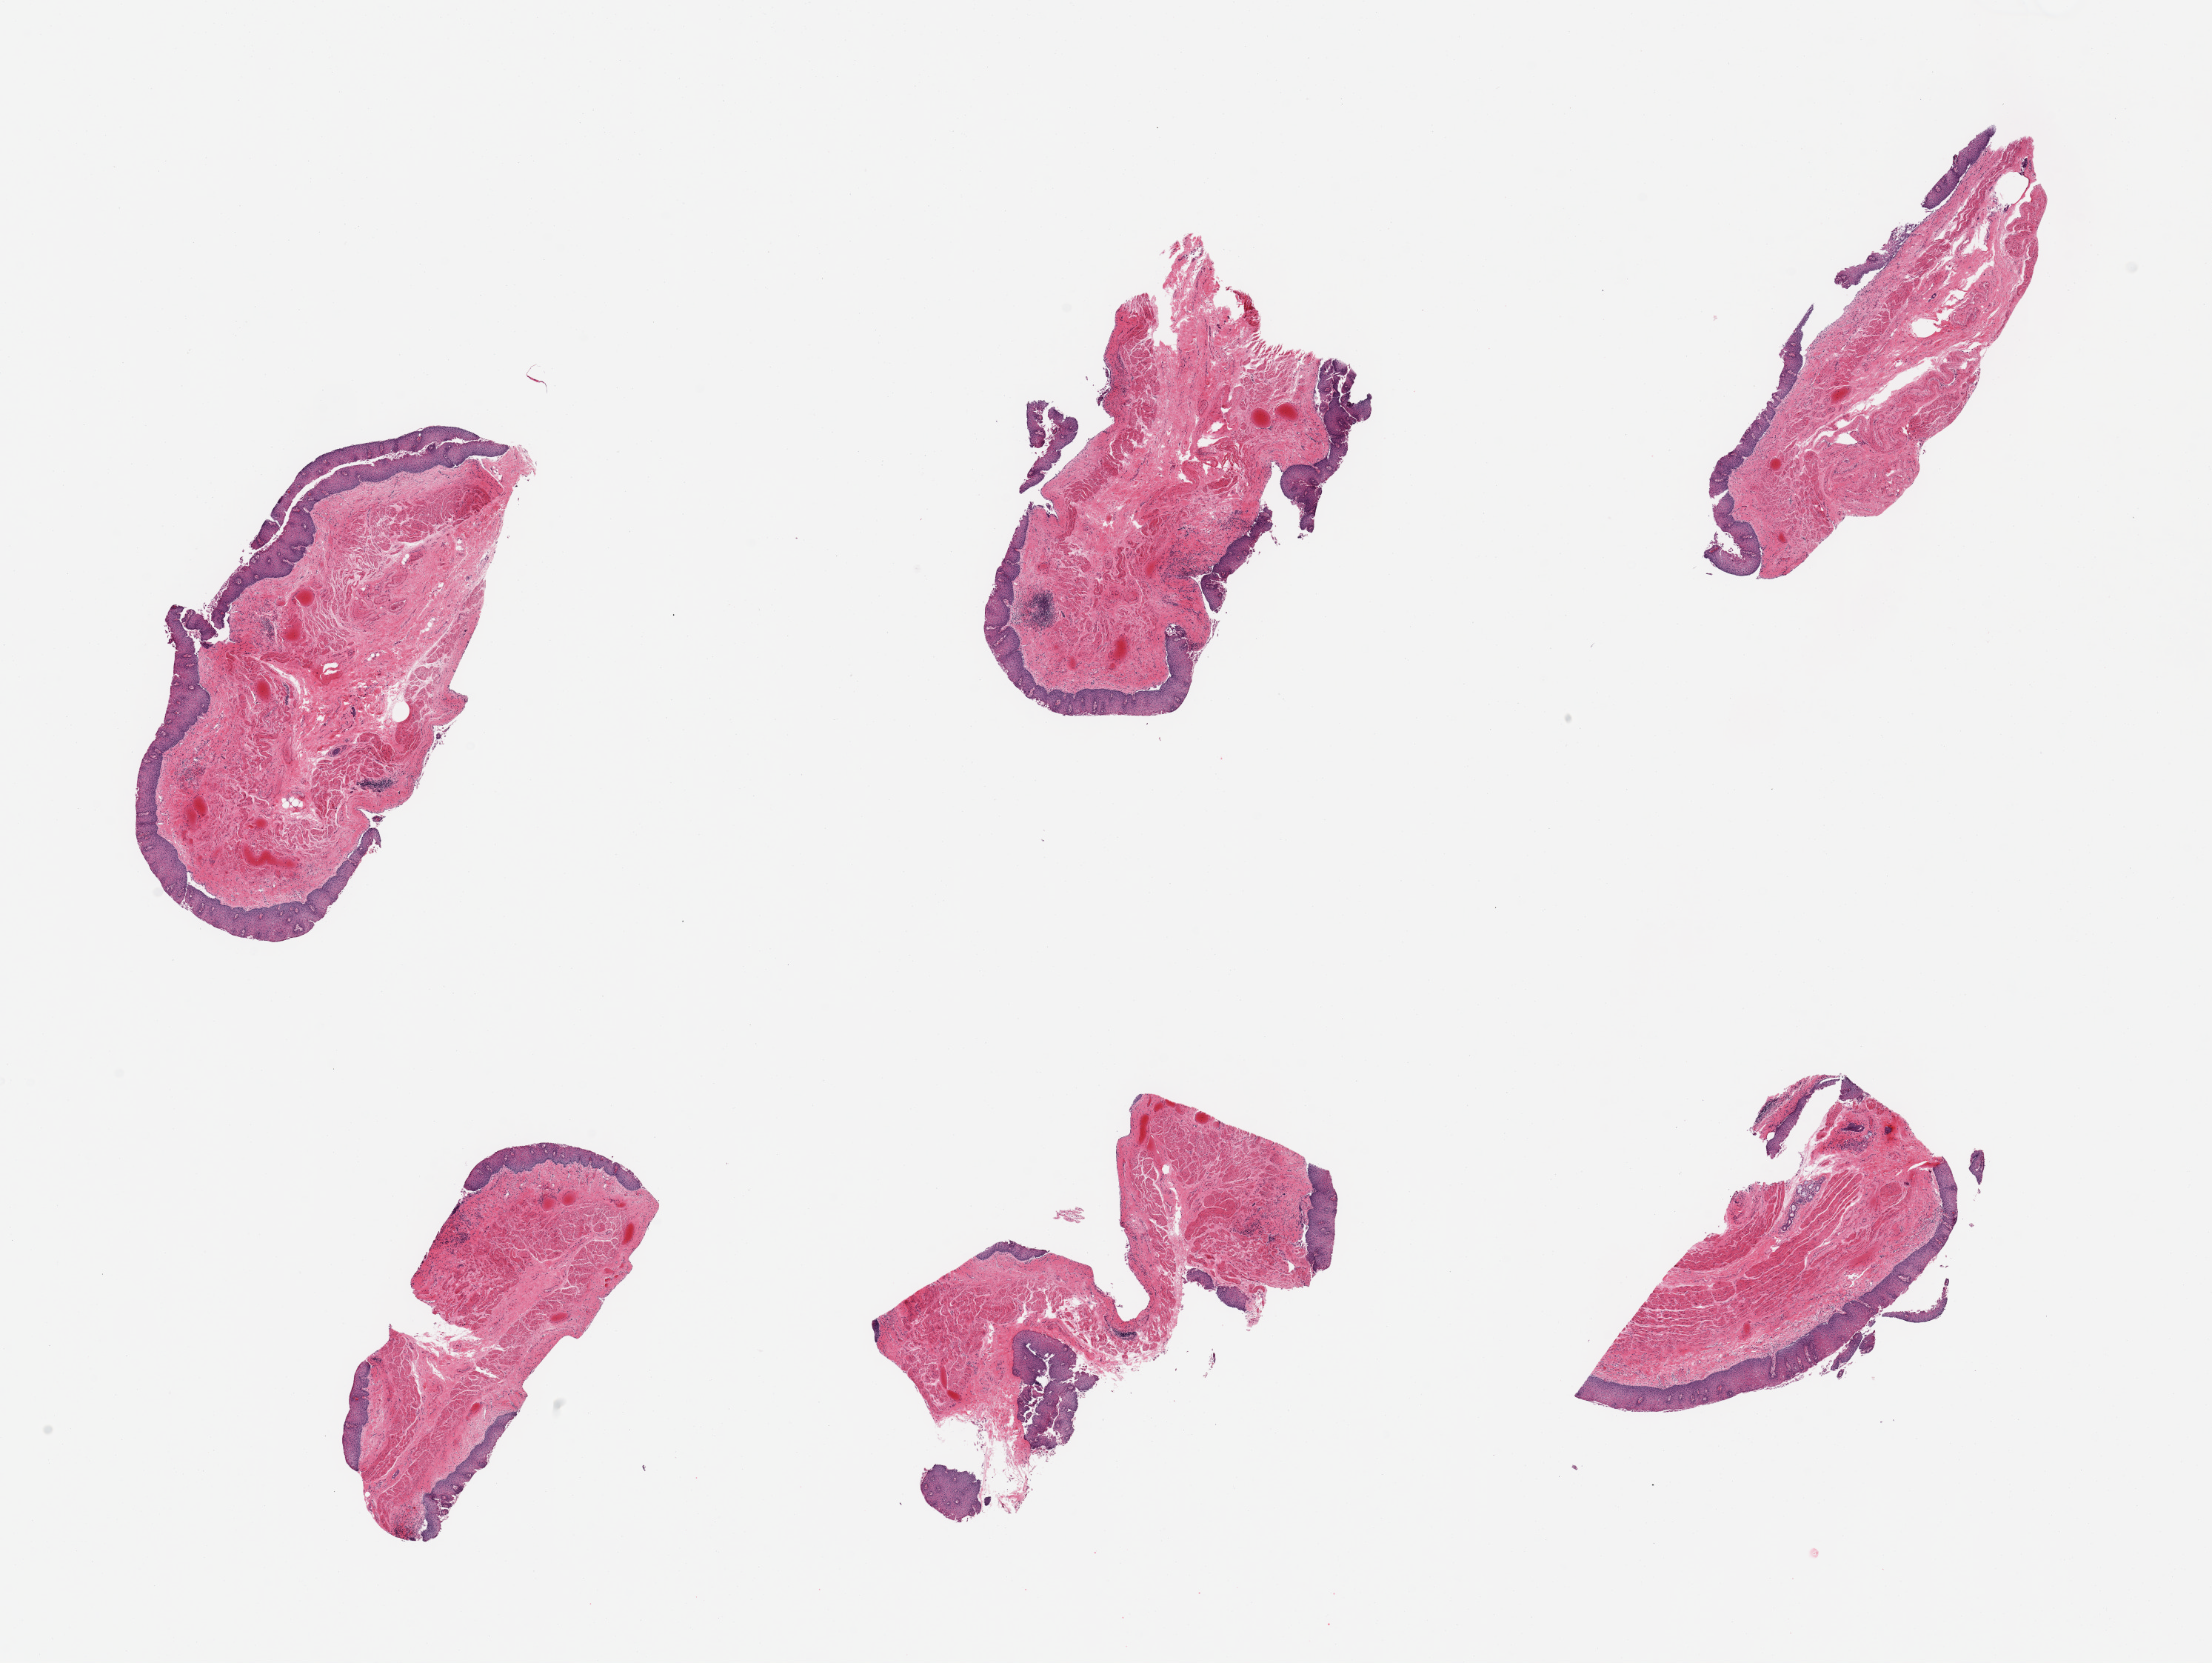
Digitized H&E-stained section, whole scanned area (about 23.6 x 17.8 mm) shown as a low-resolution overview. PAXgene-fixed paraffin-embedded (PFPE) section. Sampled site (target tissue): esophageal mucous membrane. Donor tissue sample. Donor: male.
Pathologist's review note for this sample: 6 pieces; epithelium focally fragmented.